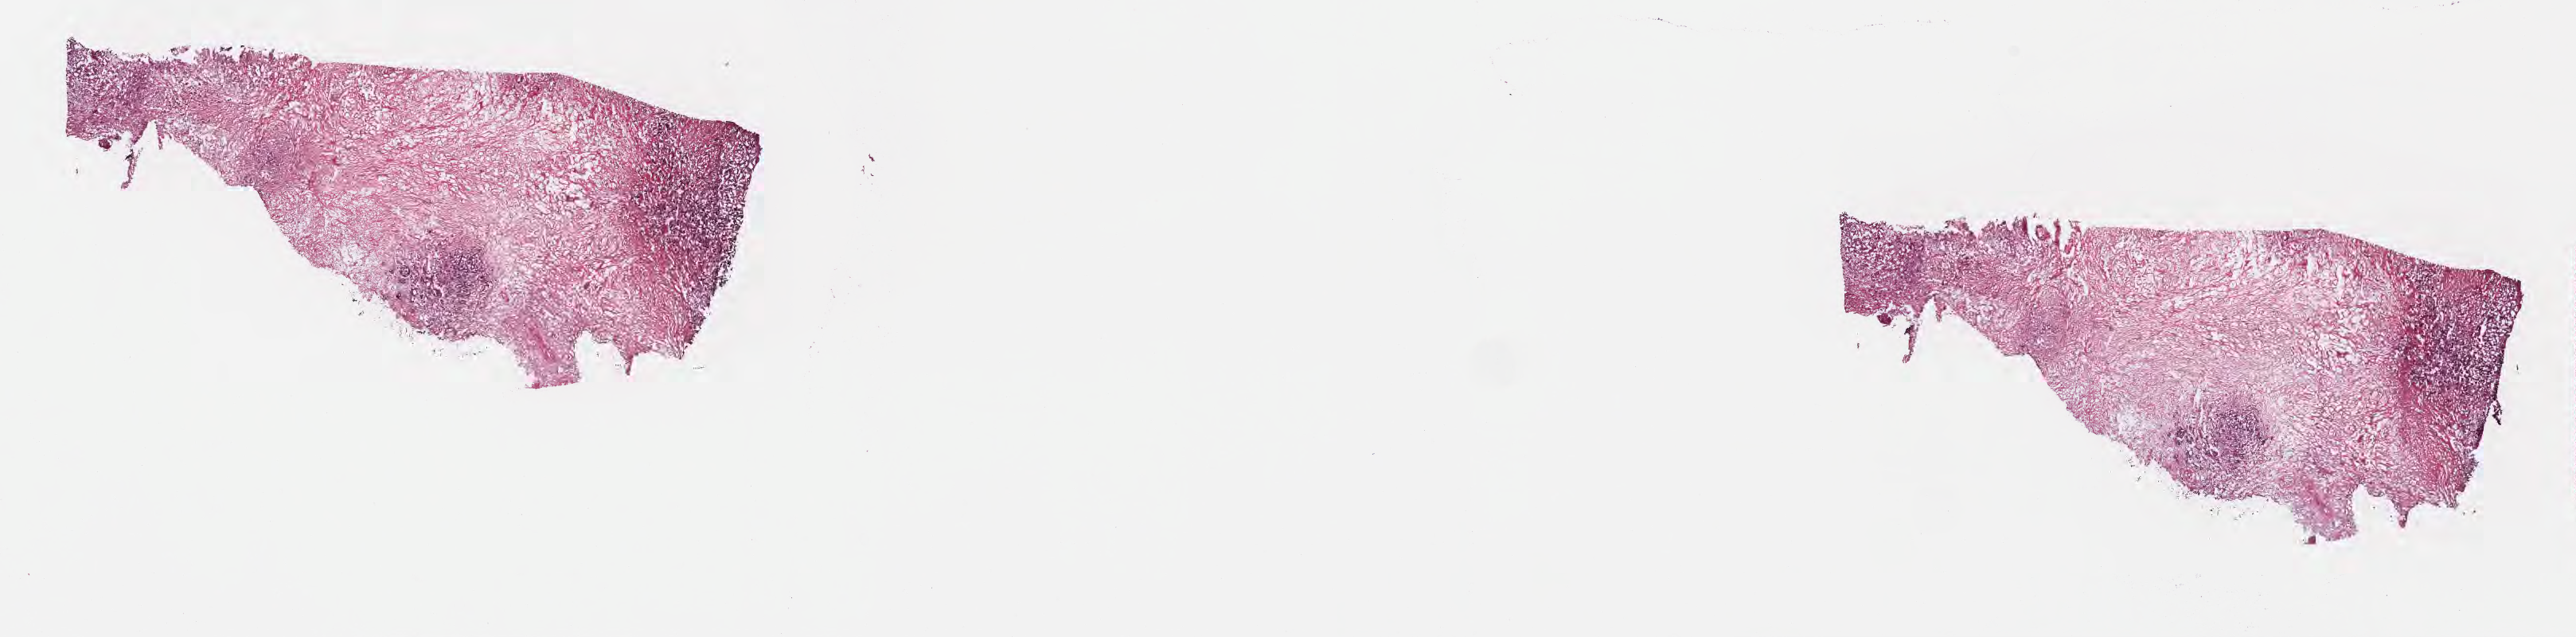
Whole-slide image, hematoxylin and eosin (H&E) stain, low-resolution overview of the scanned area, about 26.2 x 6.5 mm. Frozen section (tissue freezing medium). Specimen: primary tumor. Anatomic site: head of pancreas. Patient: female, age at initial diagnosis 46 years. Tumor grade: G2 (moderately differentiated). Composition of this section per pathologist review: tumor cells 75%, tumor nuclei 75%, stromal cells 21%, necrosis 0%, normal cells 4%. Inflammatory infiltration, as recorded: lymphocyte infiltration 4%, monocyte infiltration 2%, neutrophil infiltration 7%.
- section: bottom of the tissue portion
- diagnosis: Infiltrating duct carcinoma, NOS
- AJCC pathologic stage: Stage IIB